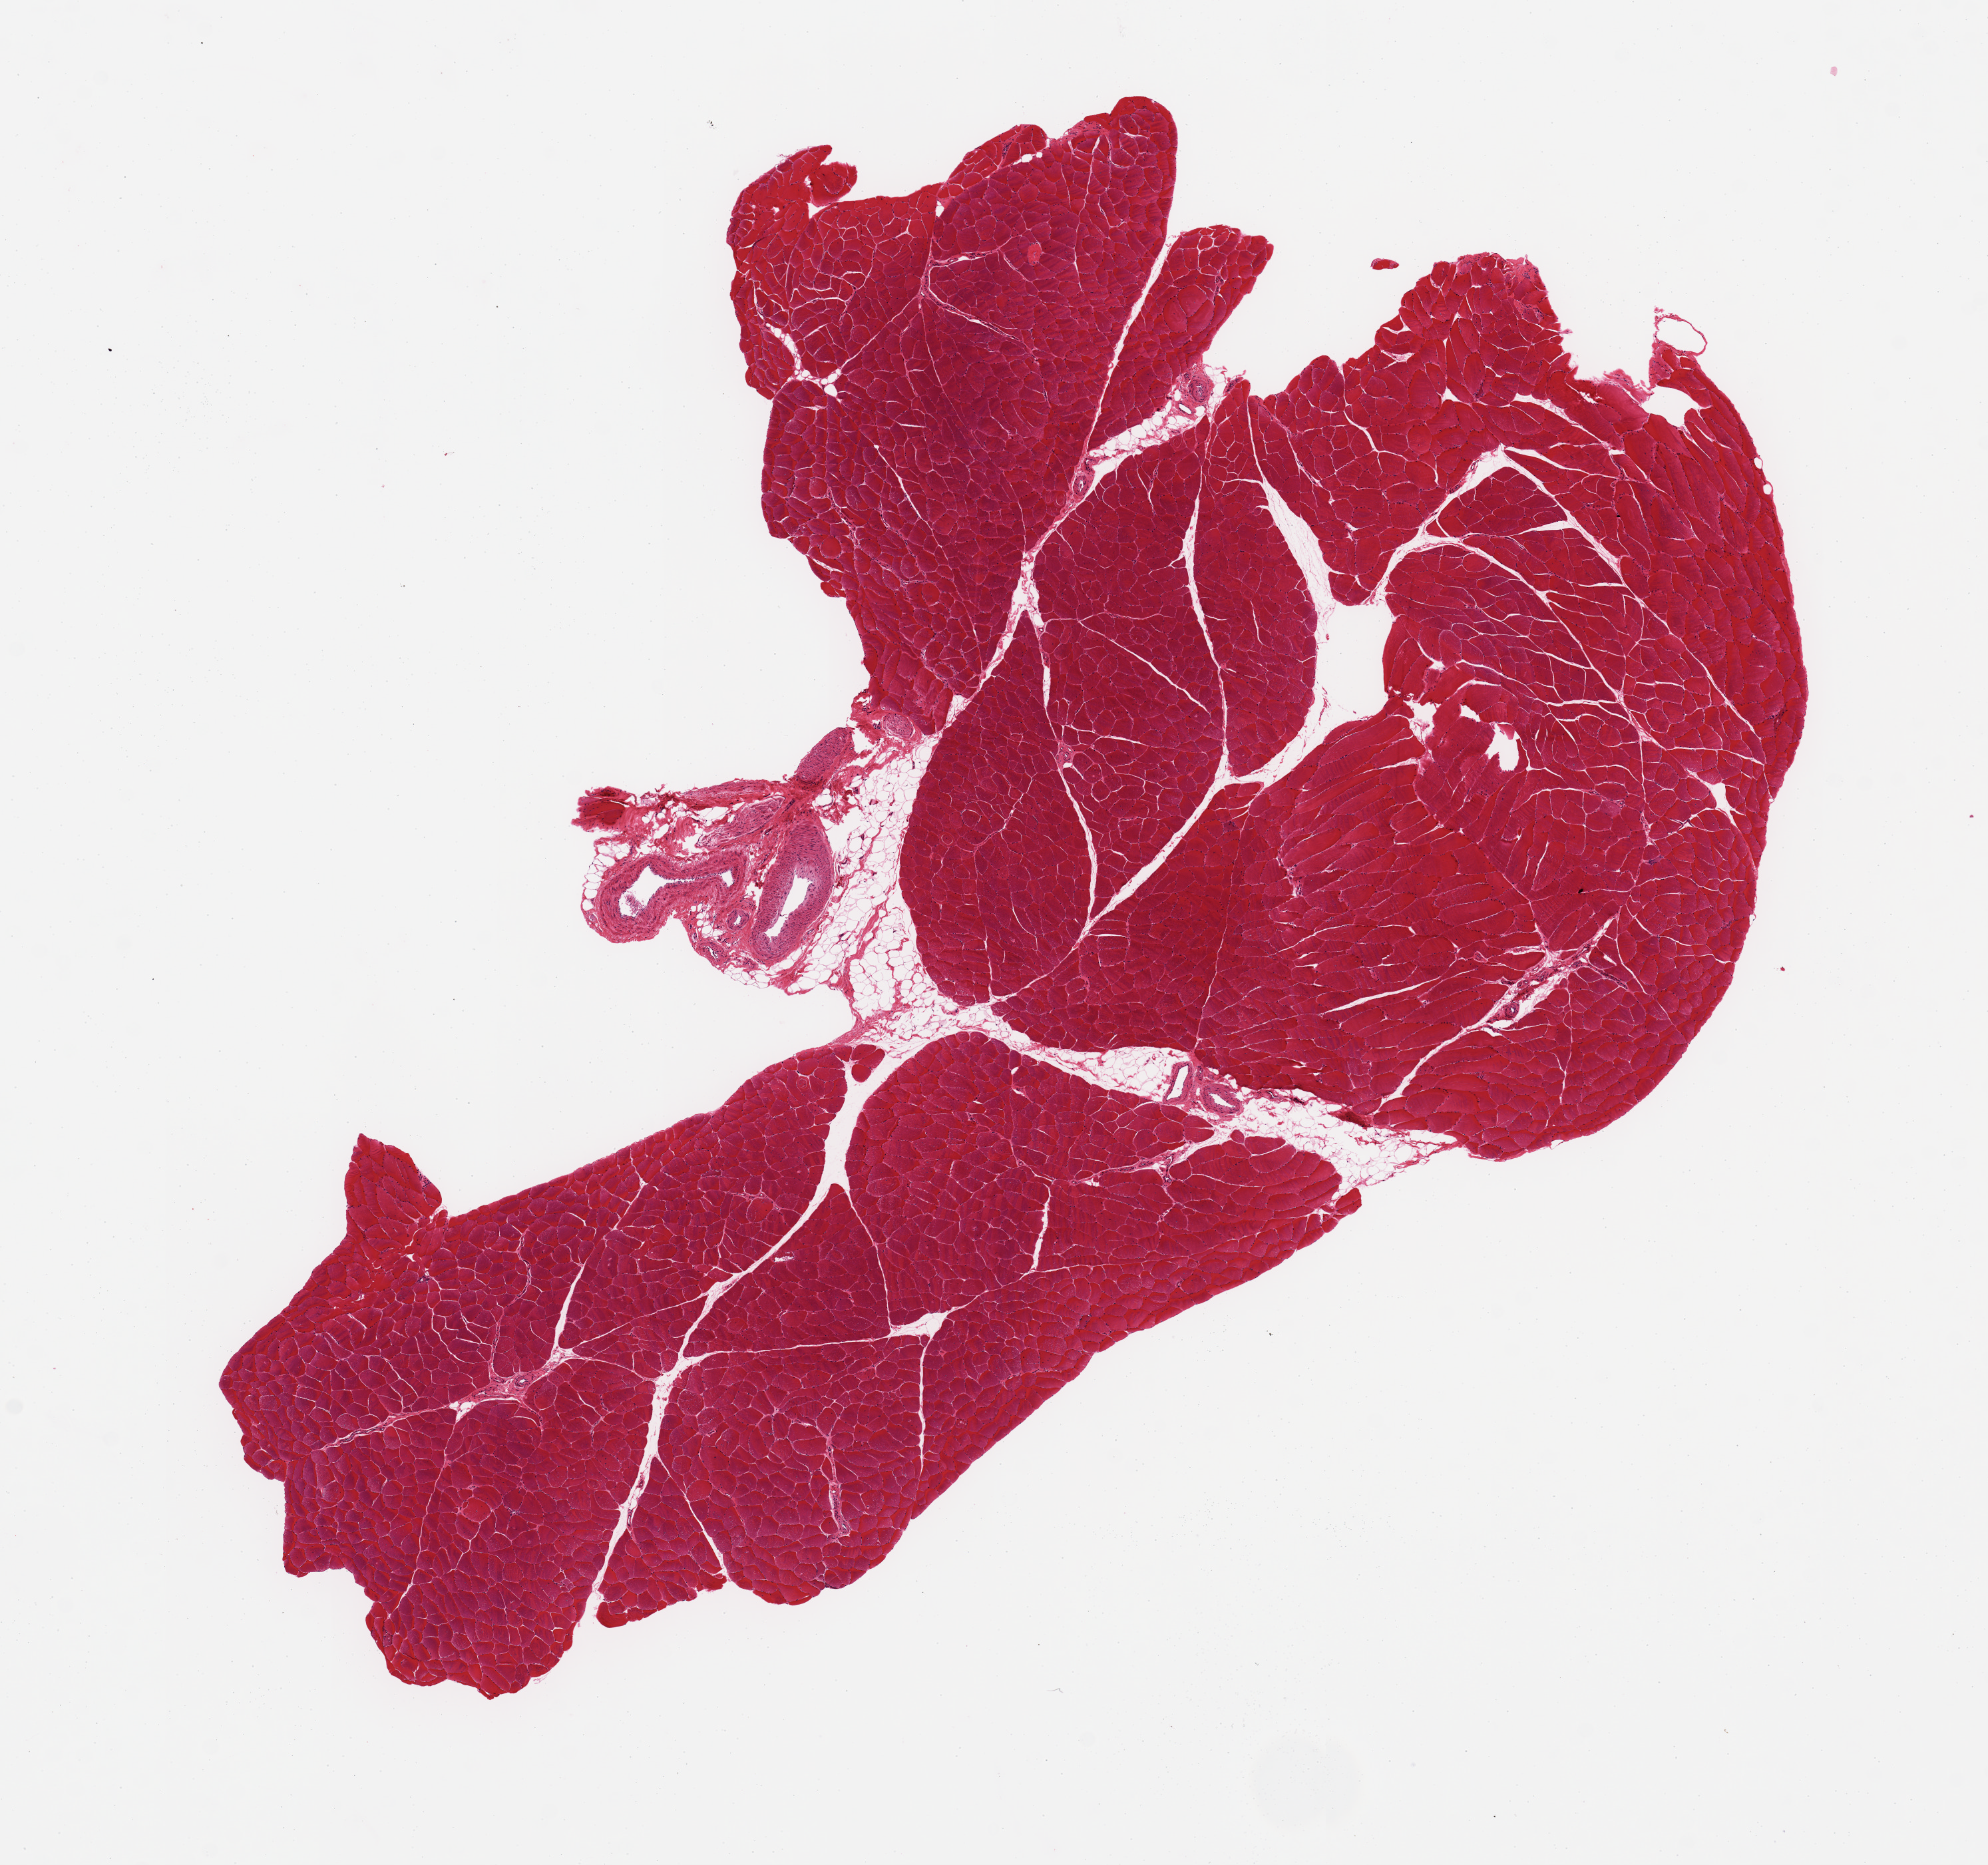
Whole-slide image, hematoxylin and eosin (H&E) stain, brightfield, a low-resolution overview of the entire scanned area, about 11.8 x 11.1 mm, PAXgene-fixed, paraffin-embedded tissue, target tissue: skeletal muscle, donor tissue sample. Donor: male.
Review note (as recorded): OK for analysis.